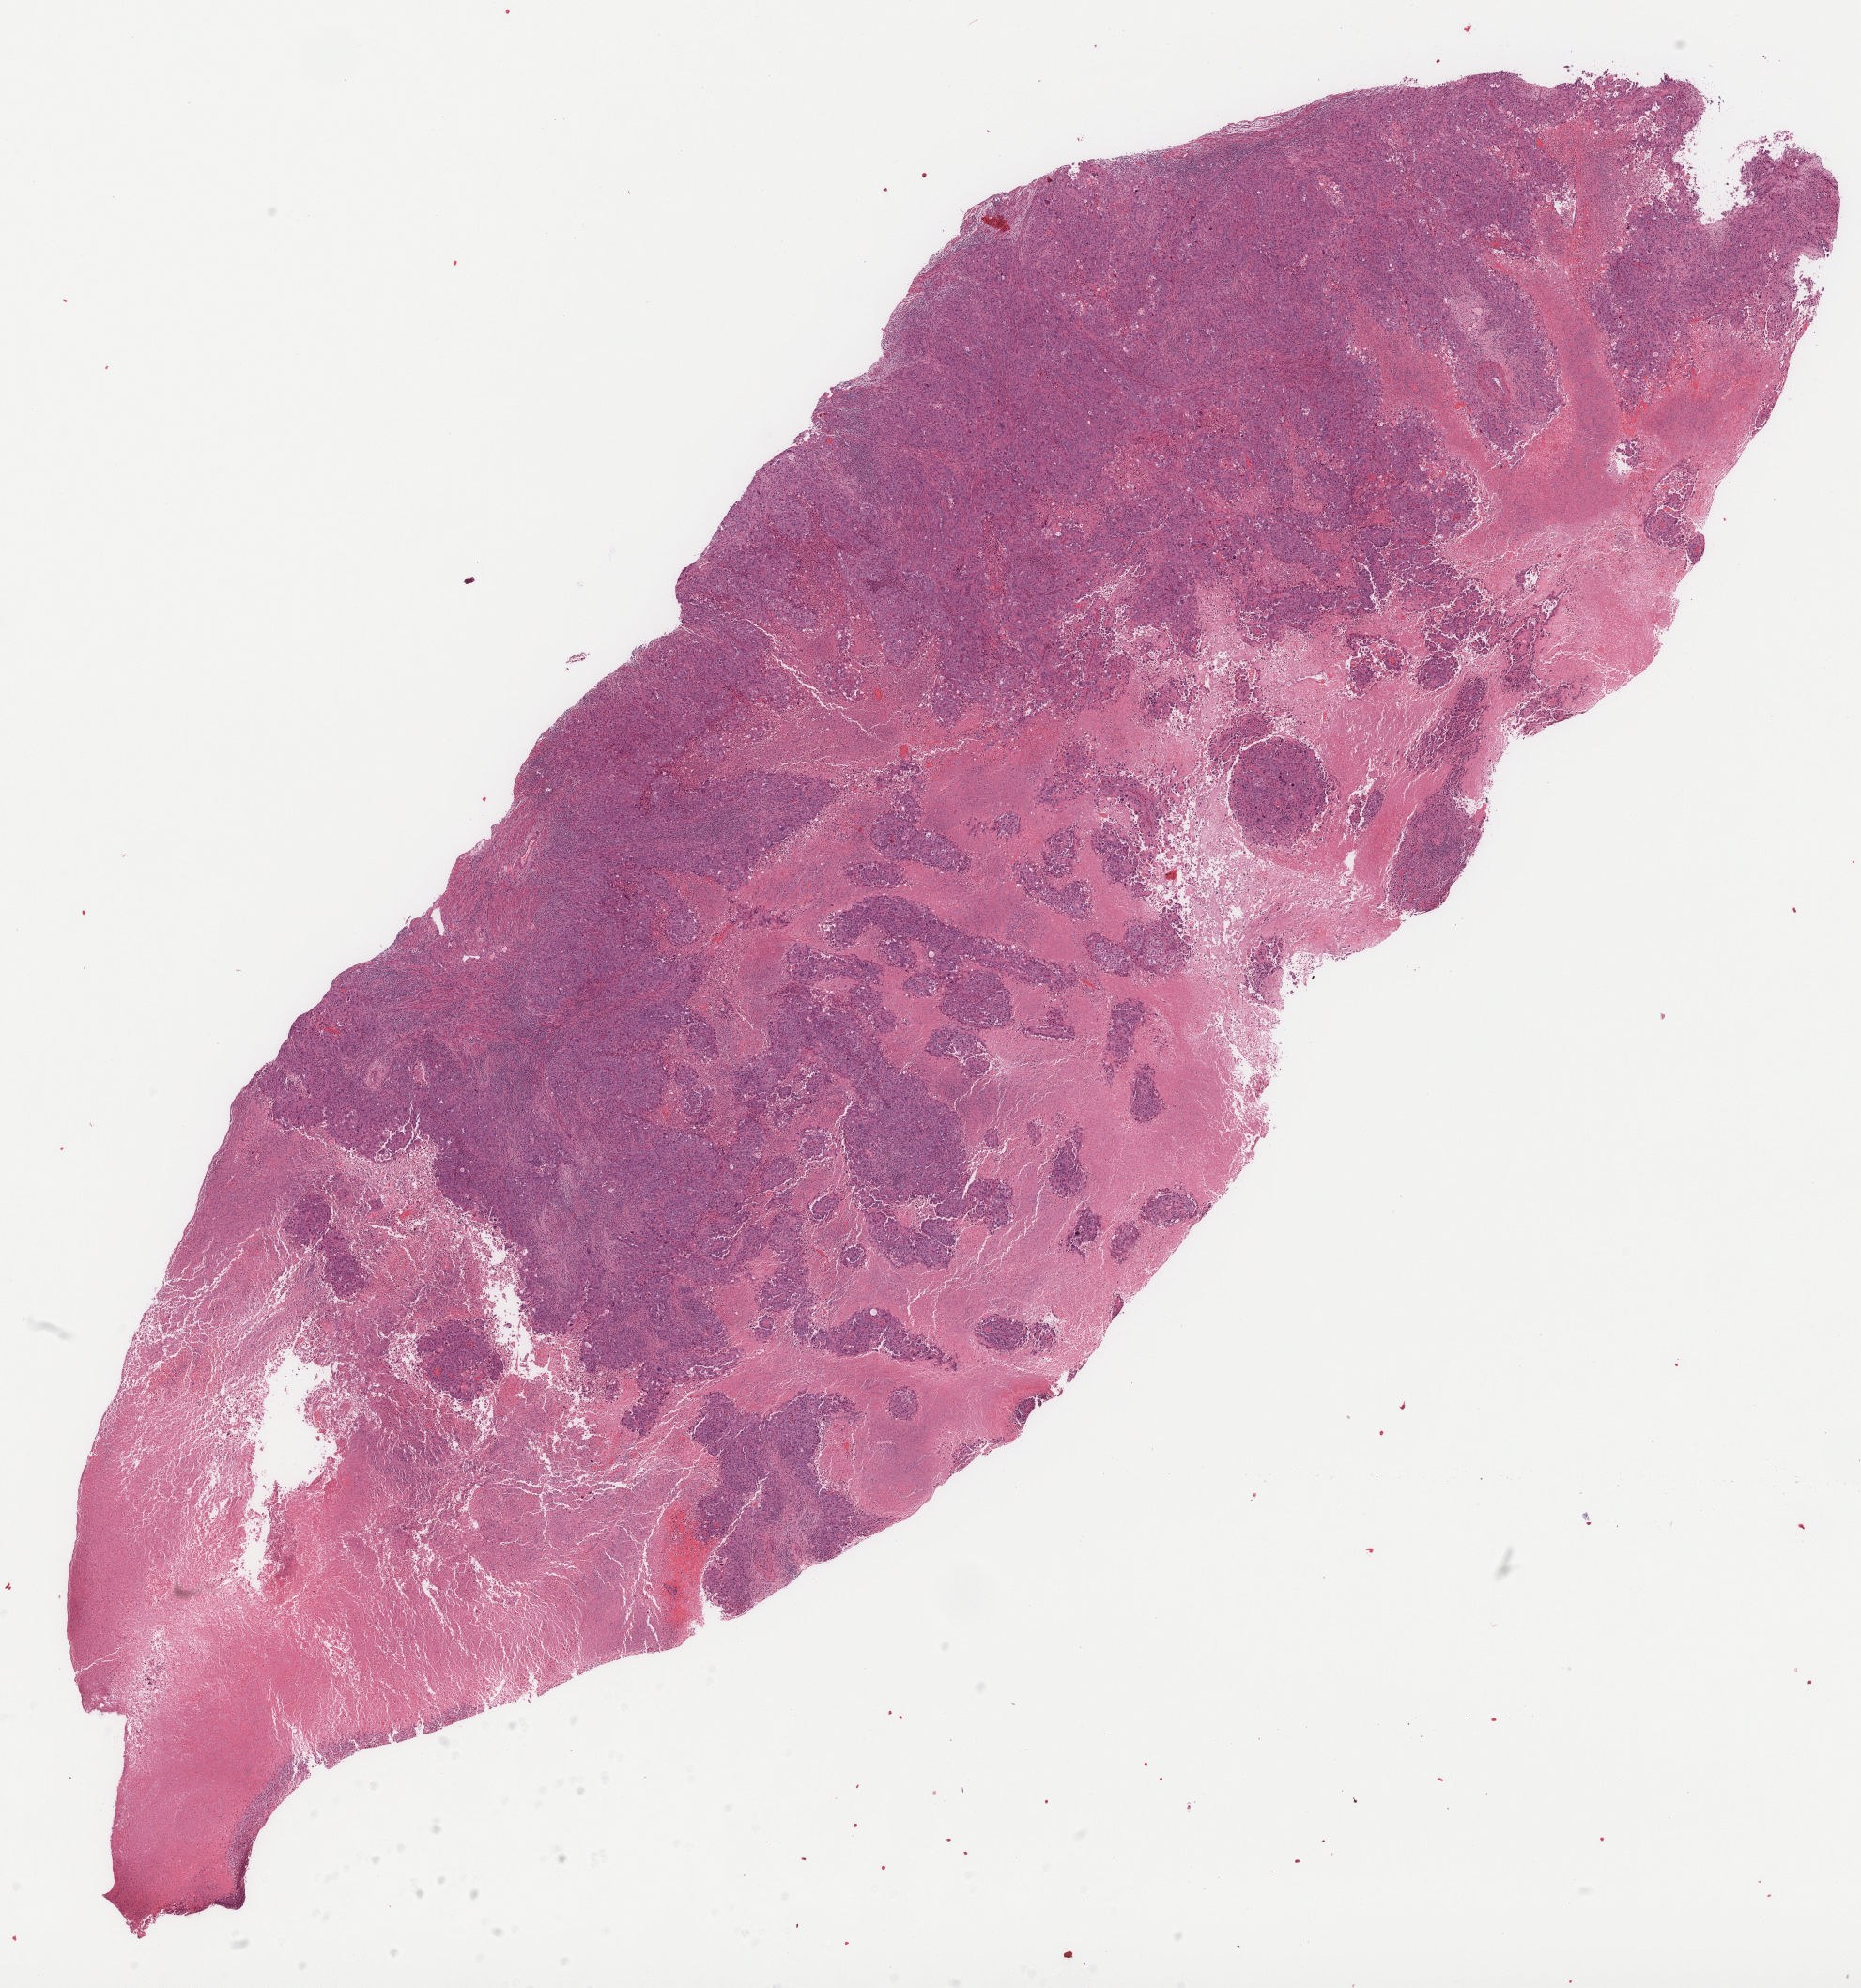
Digitized Hematoxylin and eosin (H&E) stained tissue section (whole slide) — shown as a low-resolution overview of the whole scanned area (about 16.0 x 17.1 mm, slide scanned at 40x), formalin-fixed paraffin-embedded (FFPE) diagnostic section, primary tumour sample from the uterus. Female patient; age at initial diagnosis 80 years.
Diagnosis: Serous cystadenocarcinoma, NOS (endometrium).